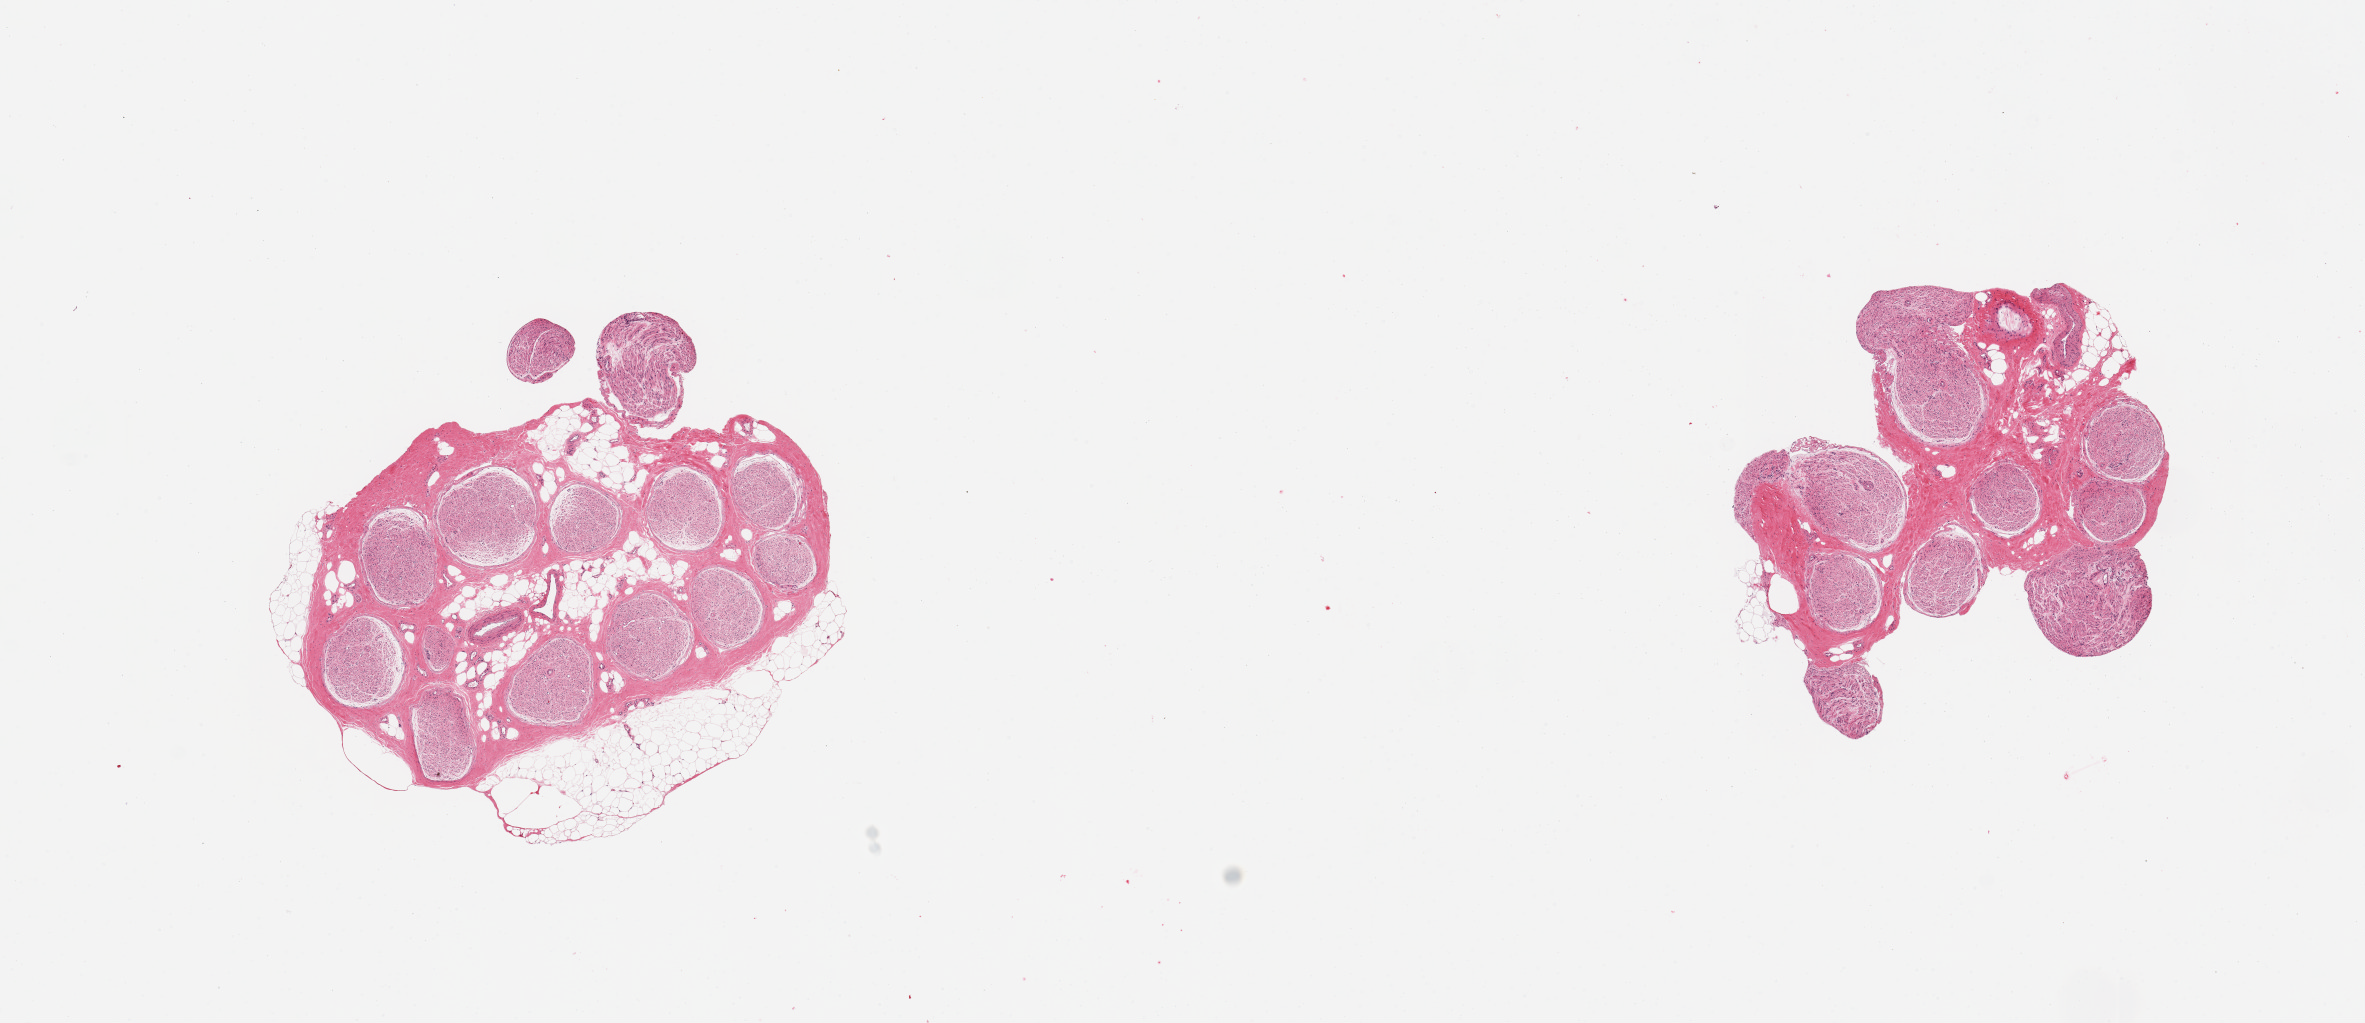
Haematoxylin and eosin whole-slide image, brightfield, low-resolution overview of the scanned area, about 18.7 x 8.1 mm. PAXgene-fixed paraffin-embedded (PFPE) section. Sampled site (target tissue): tibial nerve. Donor tissue sample. Donor sex: male.
- reviewer comment on this tissue sample: 2 pieces; less than 1mm of external fat and small amount of internal fat